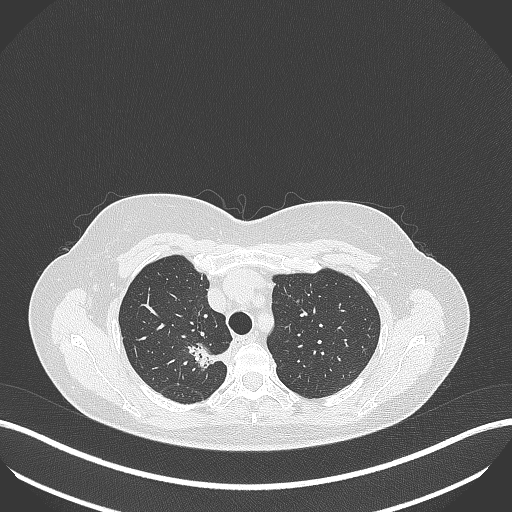
Chest CT, one axial slice. Slice 305 of 386 in the series (ordered by position). Reconstruction kernel B70f. Lung window (W 1500 / L -600 HU). 512 × 512 image matrix, field of view 400 × 400 mm. Female patient, age 65 years. Case-level facts recorded for this patient, not image findings: clinical TNM (as recorded): T1b N0 M0.
Structures marked on this image (rectangle marked by the reading radiologist):
- lung tumour (recorded histology: adenocarcinoma): box from (x=183, y=338) to (x=230, y=375) px